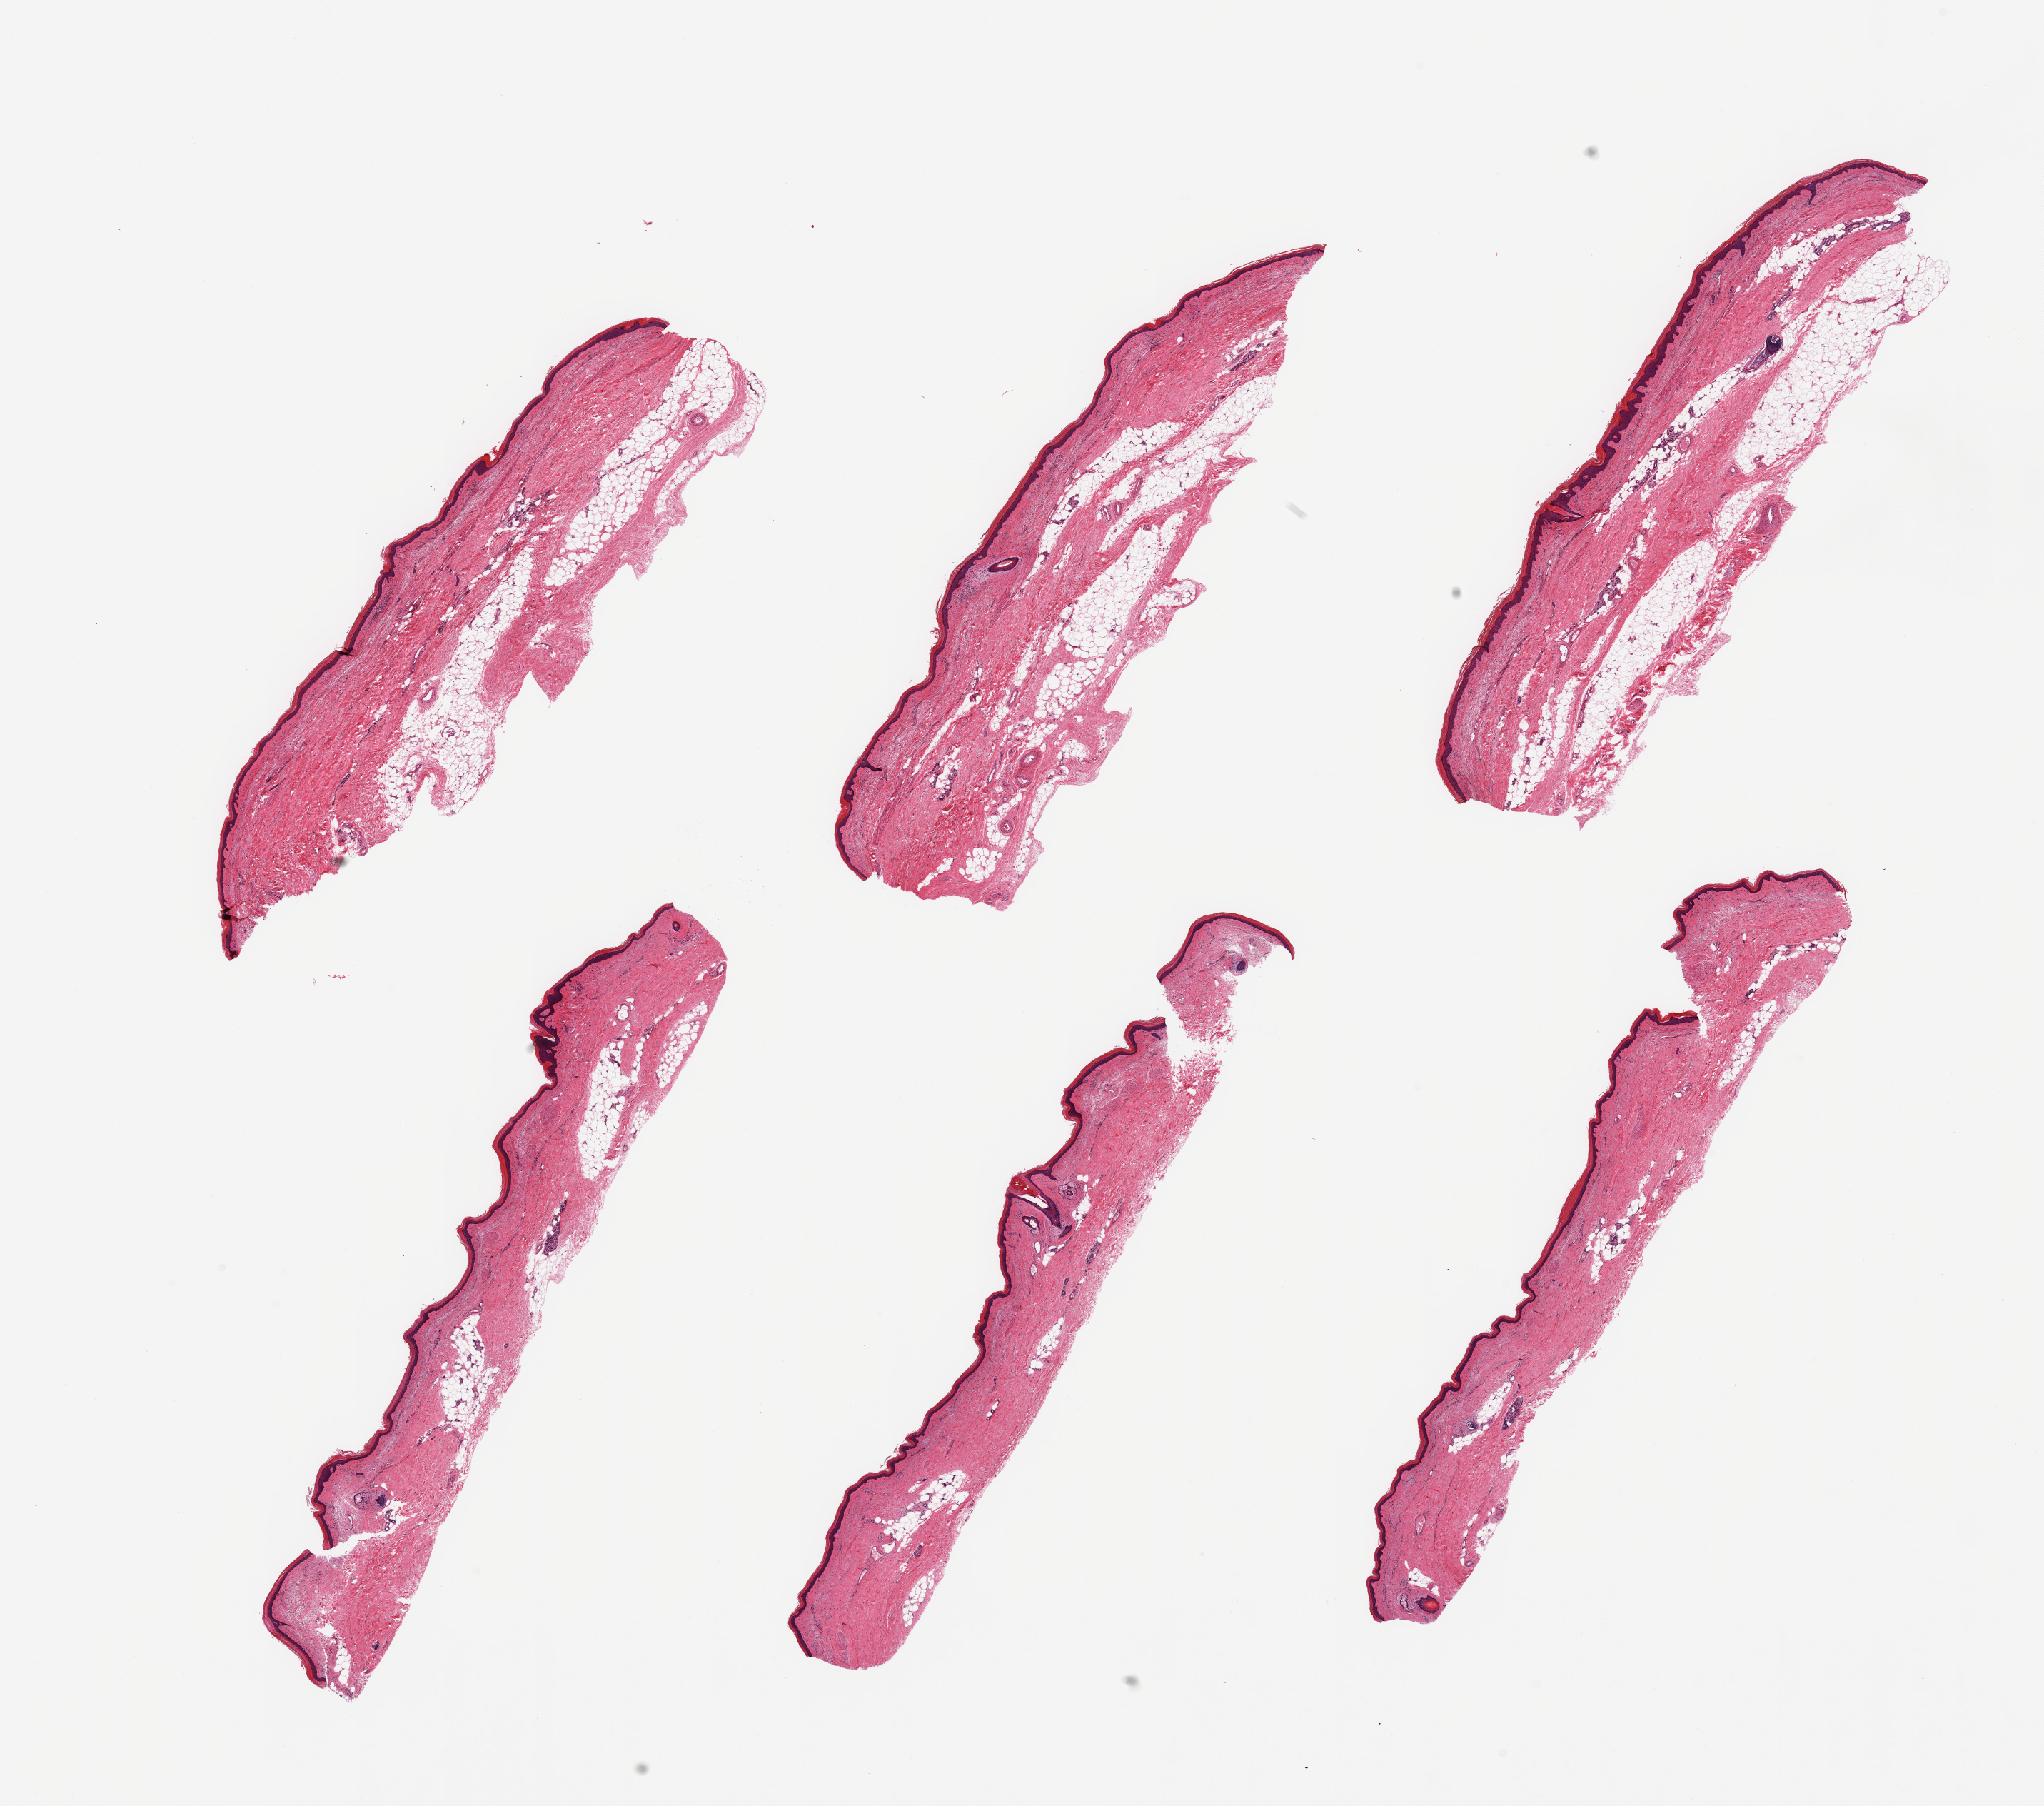
H&E whole-slide image — whole scanned area (about 22.6 x 20.0 mm) shown as a low-resolution overview. PAXgene-fixed, paraffin-embedded tissue. Target tissue: skin of lower leg. Tissue donor sample. Donor: male.
Reviewer comment on this tissue sample: 6 pieces; 10-40% dermal fat.